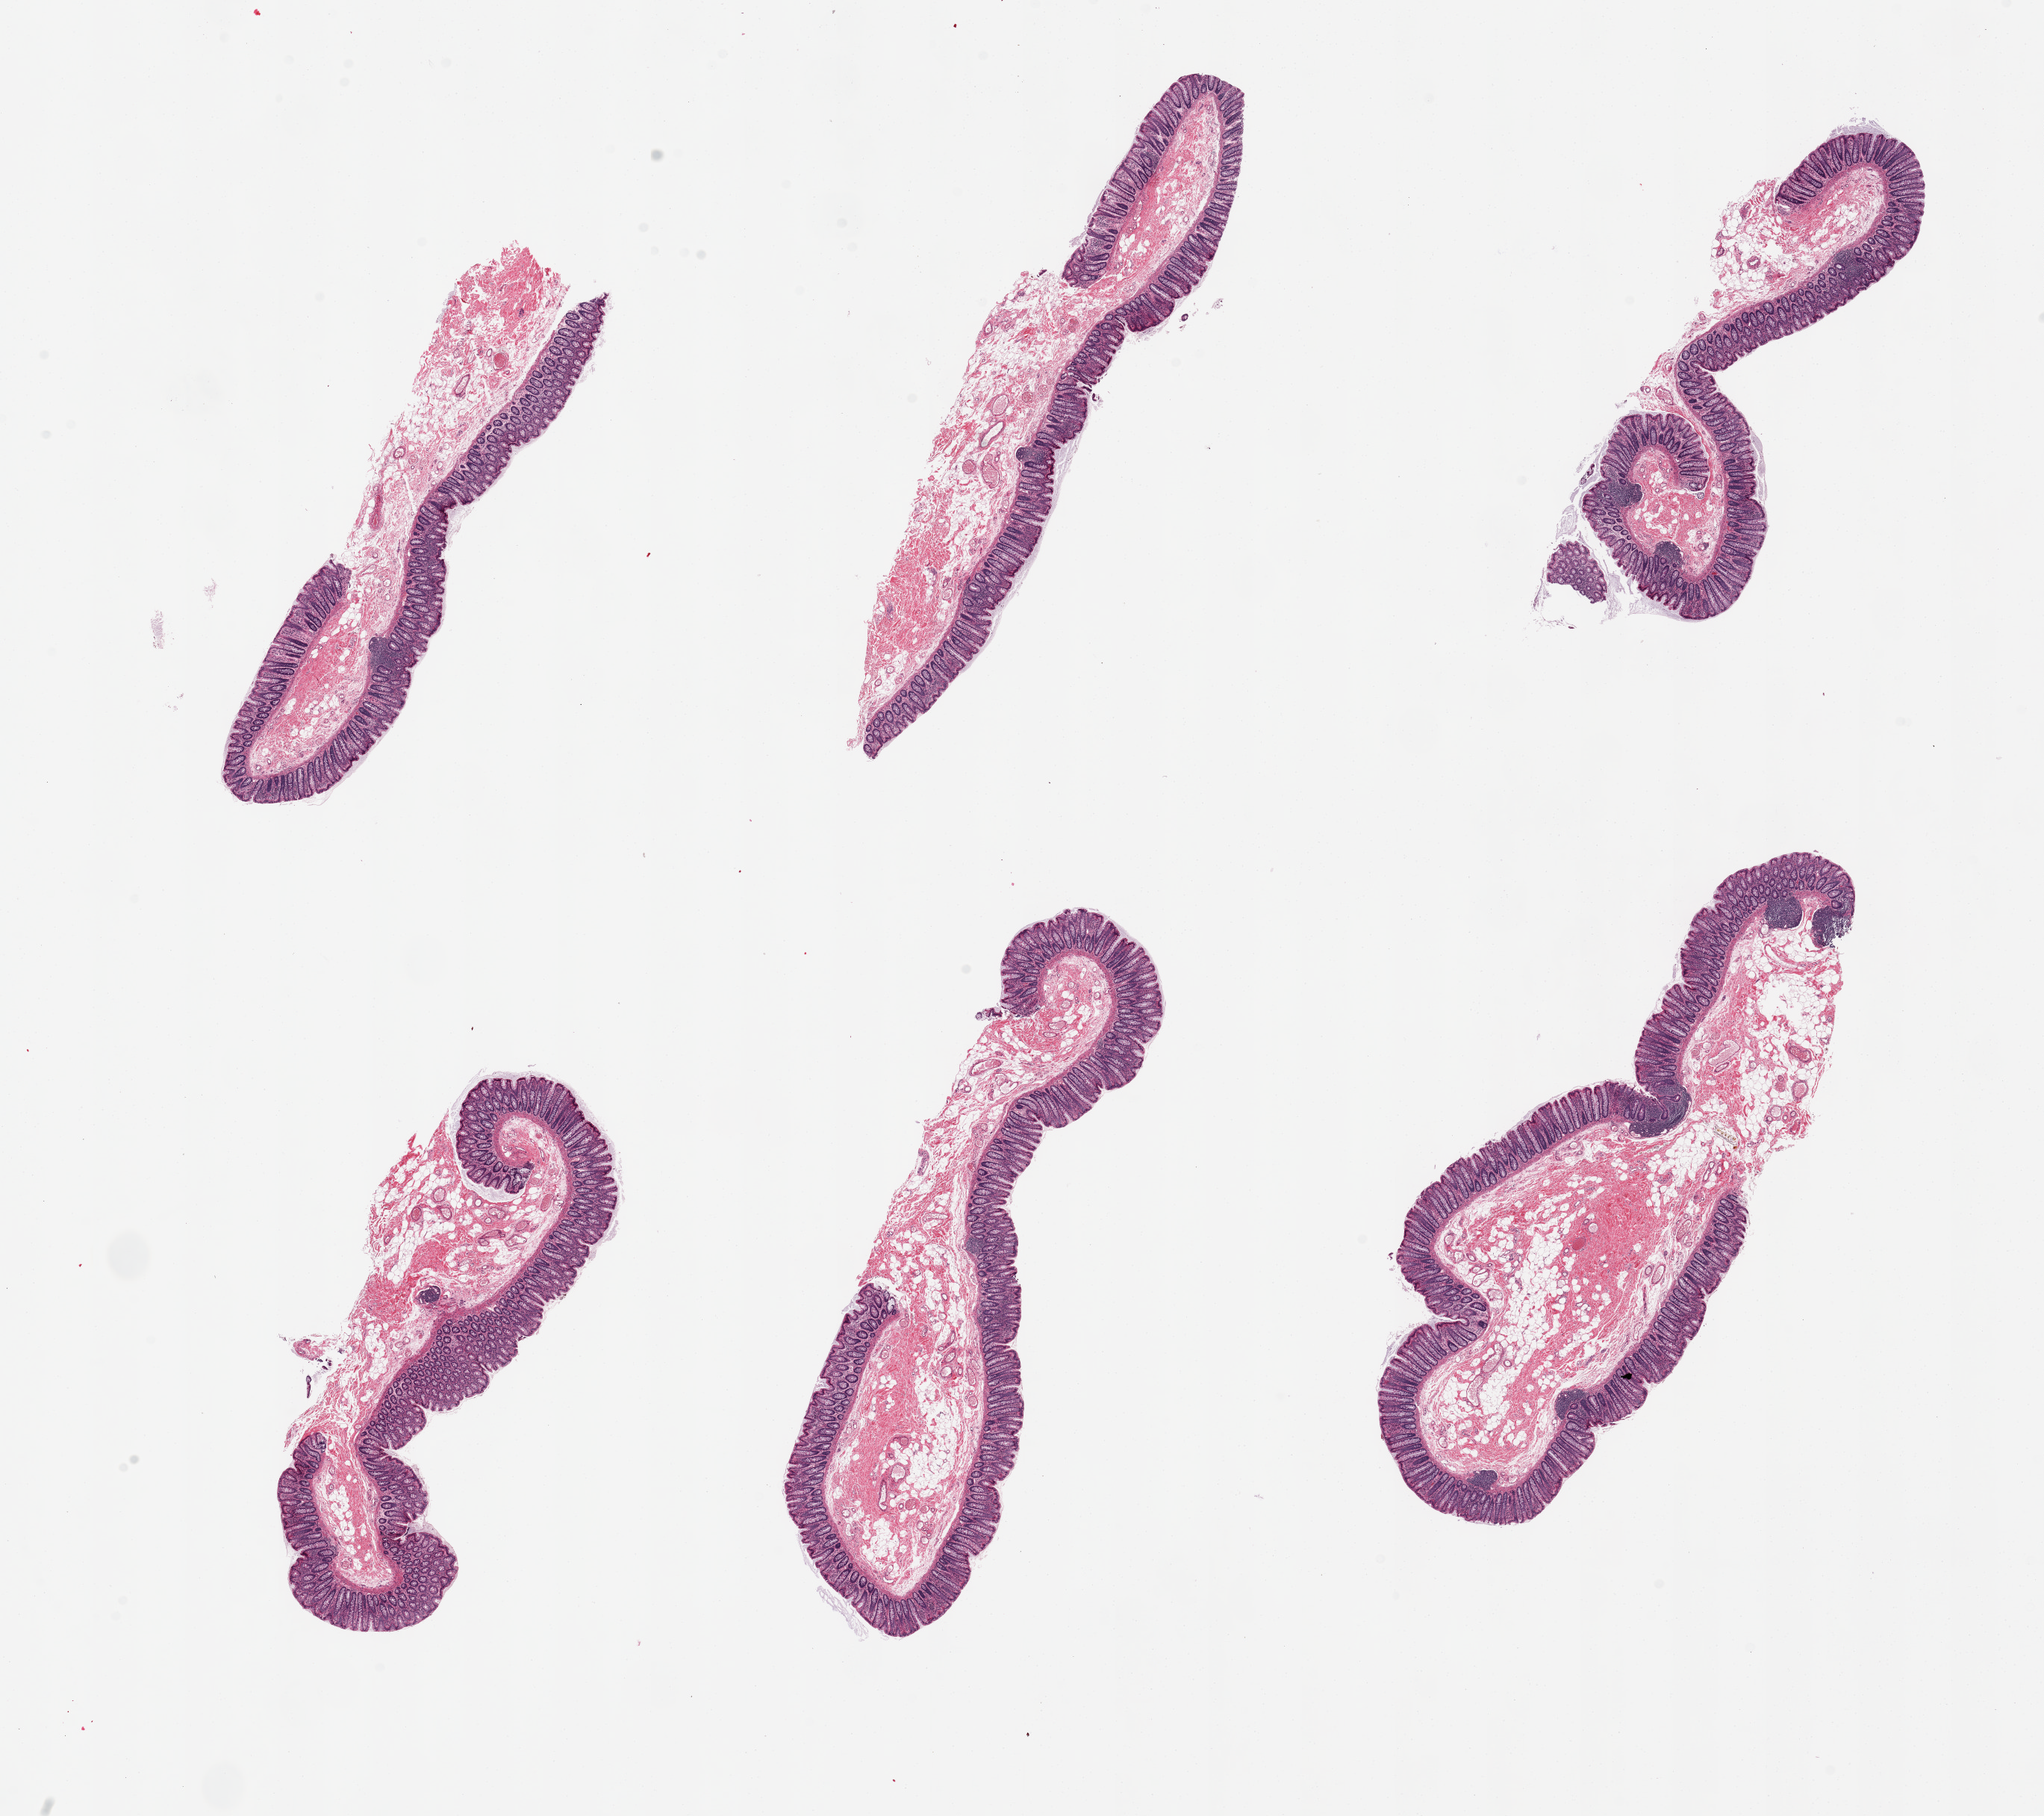
Whole-slide image, haematoxylin and eosin stain, whole scanned area (about 21.7 x 19.2 mm, slide scanned at 20x) shown as a low-resolution overview; PAXgene-fixed paraffin-embedded (PFPE) section; target tissue: transverse colon; donor tissue sample. Female donor.
Reviewer comment on this tissue sample: 6 pieces, up to 8x2mm; mucosa well preserved ~20% thickness.